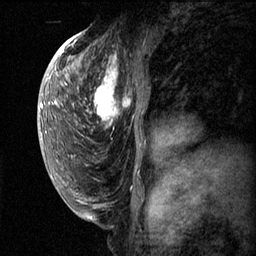
Breast MRI (dynamic contrast-enhanced), one sagittal slice; position 33 of 60 along the scan axis; dynamic contrast-enhanced series, image 2 of 3 at this slice position (ordered by acquisition); 1.5 T; TE 4.2 ms, TR 11.1 ms; 2 mm slice thickness; 256 × 256 image matrix, field of view 180 × 180 mm. Female patient, age 50 years.
Structures marked on this image (semi-automatically segmented with operator editing):
- analysis volume of interest (the breast-tissue region the enhancement analysis was run in; not a lesion): bounding box [x1, y1, x2, y2] px = [82, 56, 150, 143]
- tumour enhancement mask (voxels above the 70 % enhancement threshold inside the analysis volume of interest): [87, 62, 138, 127]